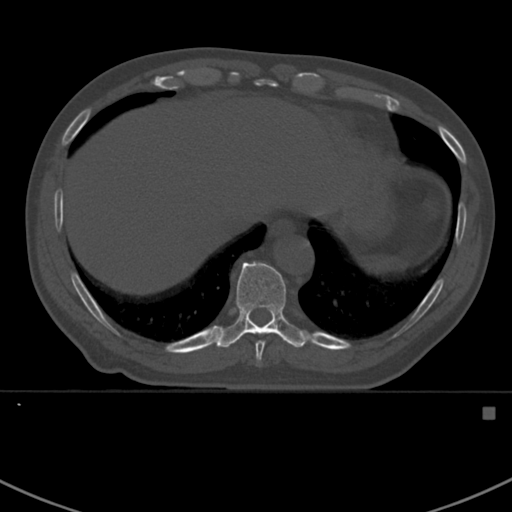
CT including the spine, one axial slice. Slice 370 of 412 in the series (ordered by position). Reconstruction kernel Br40s. 120 kVp. Bone window (W 1800 / L 400 HU). 1.5 mm slice thickness. 512 × 512 image matrix. Male patient, age 59 years. Case-level facts recorded for this patient, not image findings: primary cancer: prostate.
Structures marked on this image (semi-automatically segmented with operator editing):
- T10 vertebra: bounding box <214,262,308,348> (left, top, right, bottom; pixels)
- T9 vertebra: <255,341,265,365>